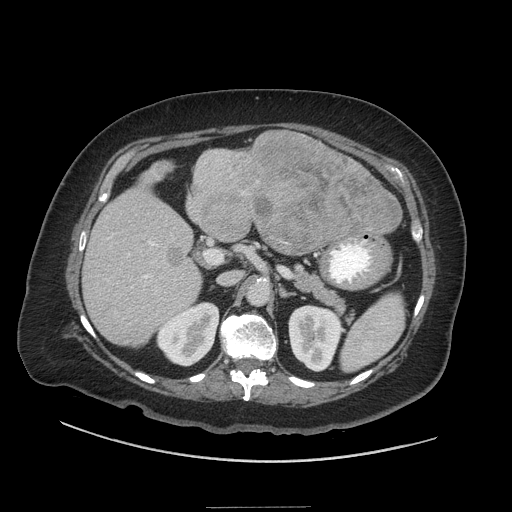
Contrast-enhanced abdominal CT (liver protocol), one axial slice. Soft-tissue window (W 400 / L 40 HU). 2.5 mm slice thickness. 512 × 512 image matrix, field of view 440 × 440 mm. From the clinical record (not read from this slice): diagnosis: hepatocellular carcinoma (patient treated with transarterial chemoembolisation; whether this scan precedes or follows treatment is not stated here); TNM stage (as recorded): Stage-II; Child-Pugh class: A; tumour differentiation: moderately differentiated; tumour nodularity: multinodular.
Structures marked on this image (semi-automatically segmented with operator editing):
- liver parenchyma outside the tumour (the mass and vessels are separate outlines, so this box may not span the whole liver): bounding box <82,142,392,346> (left, top, right, bottom; pixels)
- mass: <165,130,402,269>
- liver vessels: <107,236,176,288>